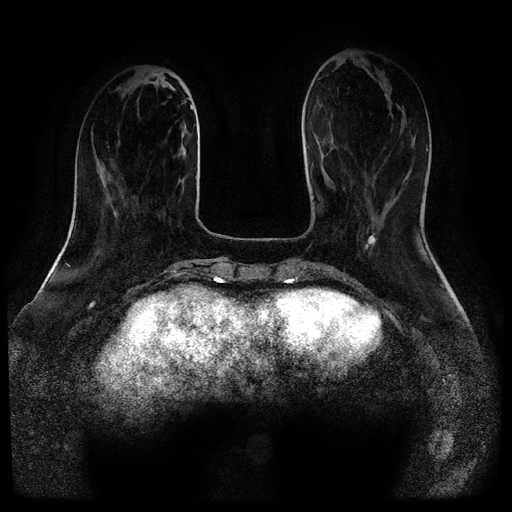
Breast MRI (dynamic contrast-enhanced, multi-phase), one axial slice. Slice 32 of 116 in the series (ordered by position). Dynamic contrast-enhanced series, time point 2 of 5 at this slice position (early post-contrast). 1.5 T. TE 2.6 ms, TR 5.3 ms. 512 × 512 image matrix, field of view 360 × 360 mm. Patient: female, 52 years.
Outlined on this slice (semi-automatic segmentation, software-assisted and operator-edited):
- breast lesion (labelled 'tumour' in the annotation; benign lesions carry a separate 'benign' label): bounding box (x1, y1, x2, y2) in pixels: (365, 232, 376, 249)